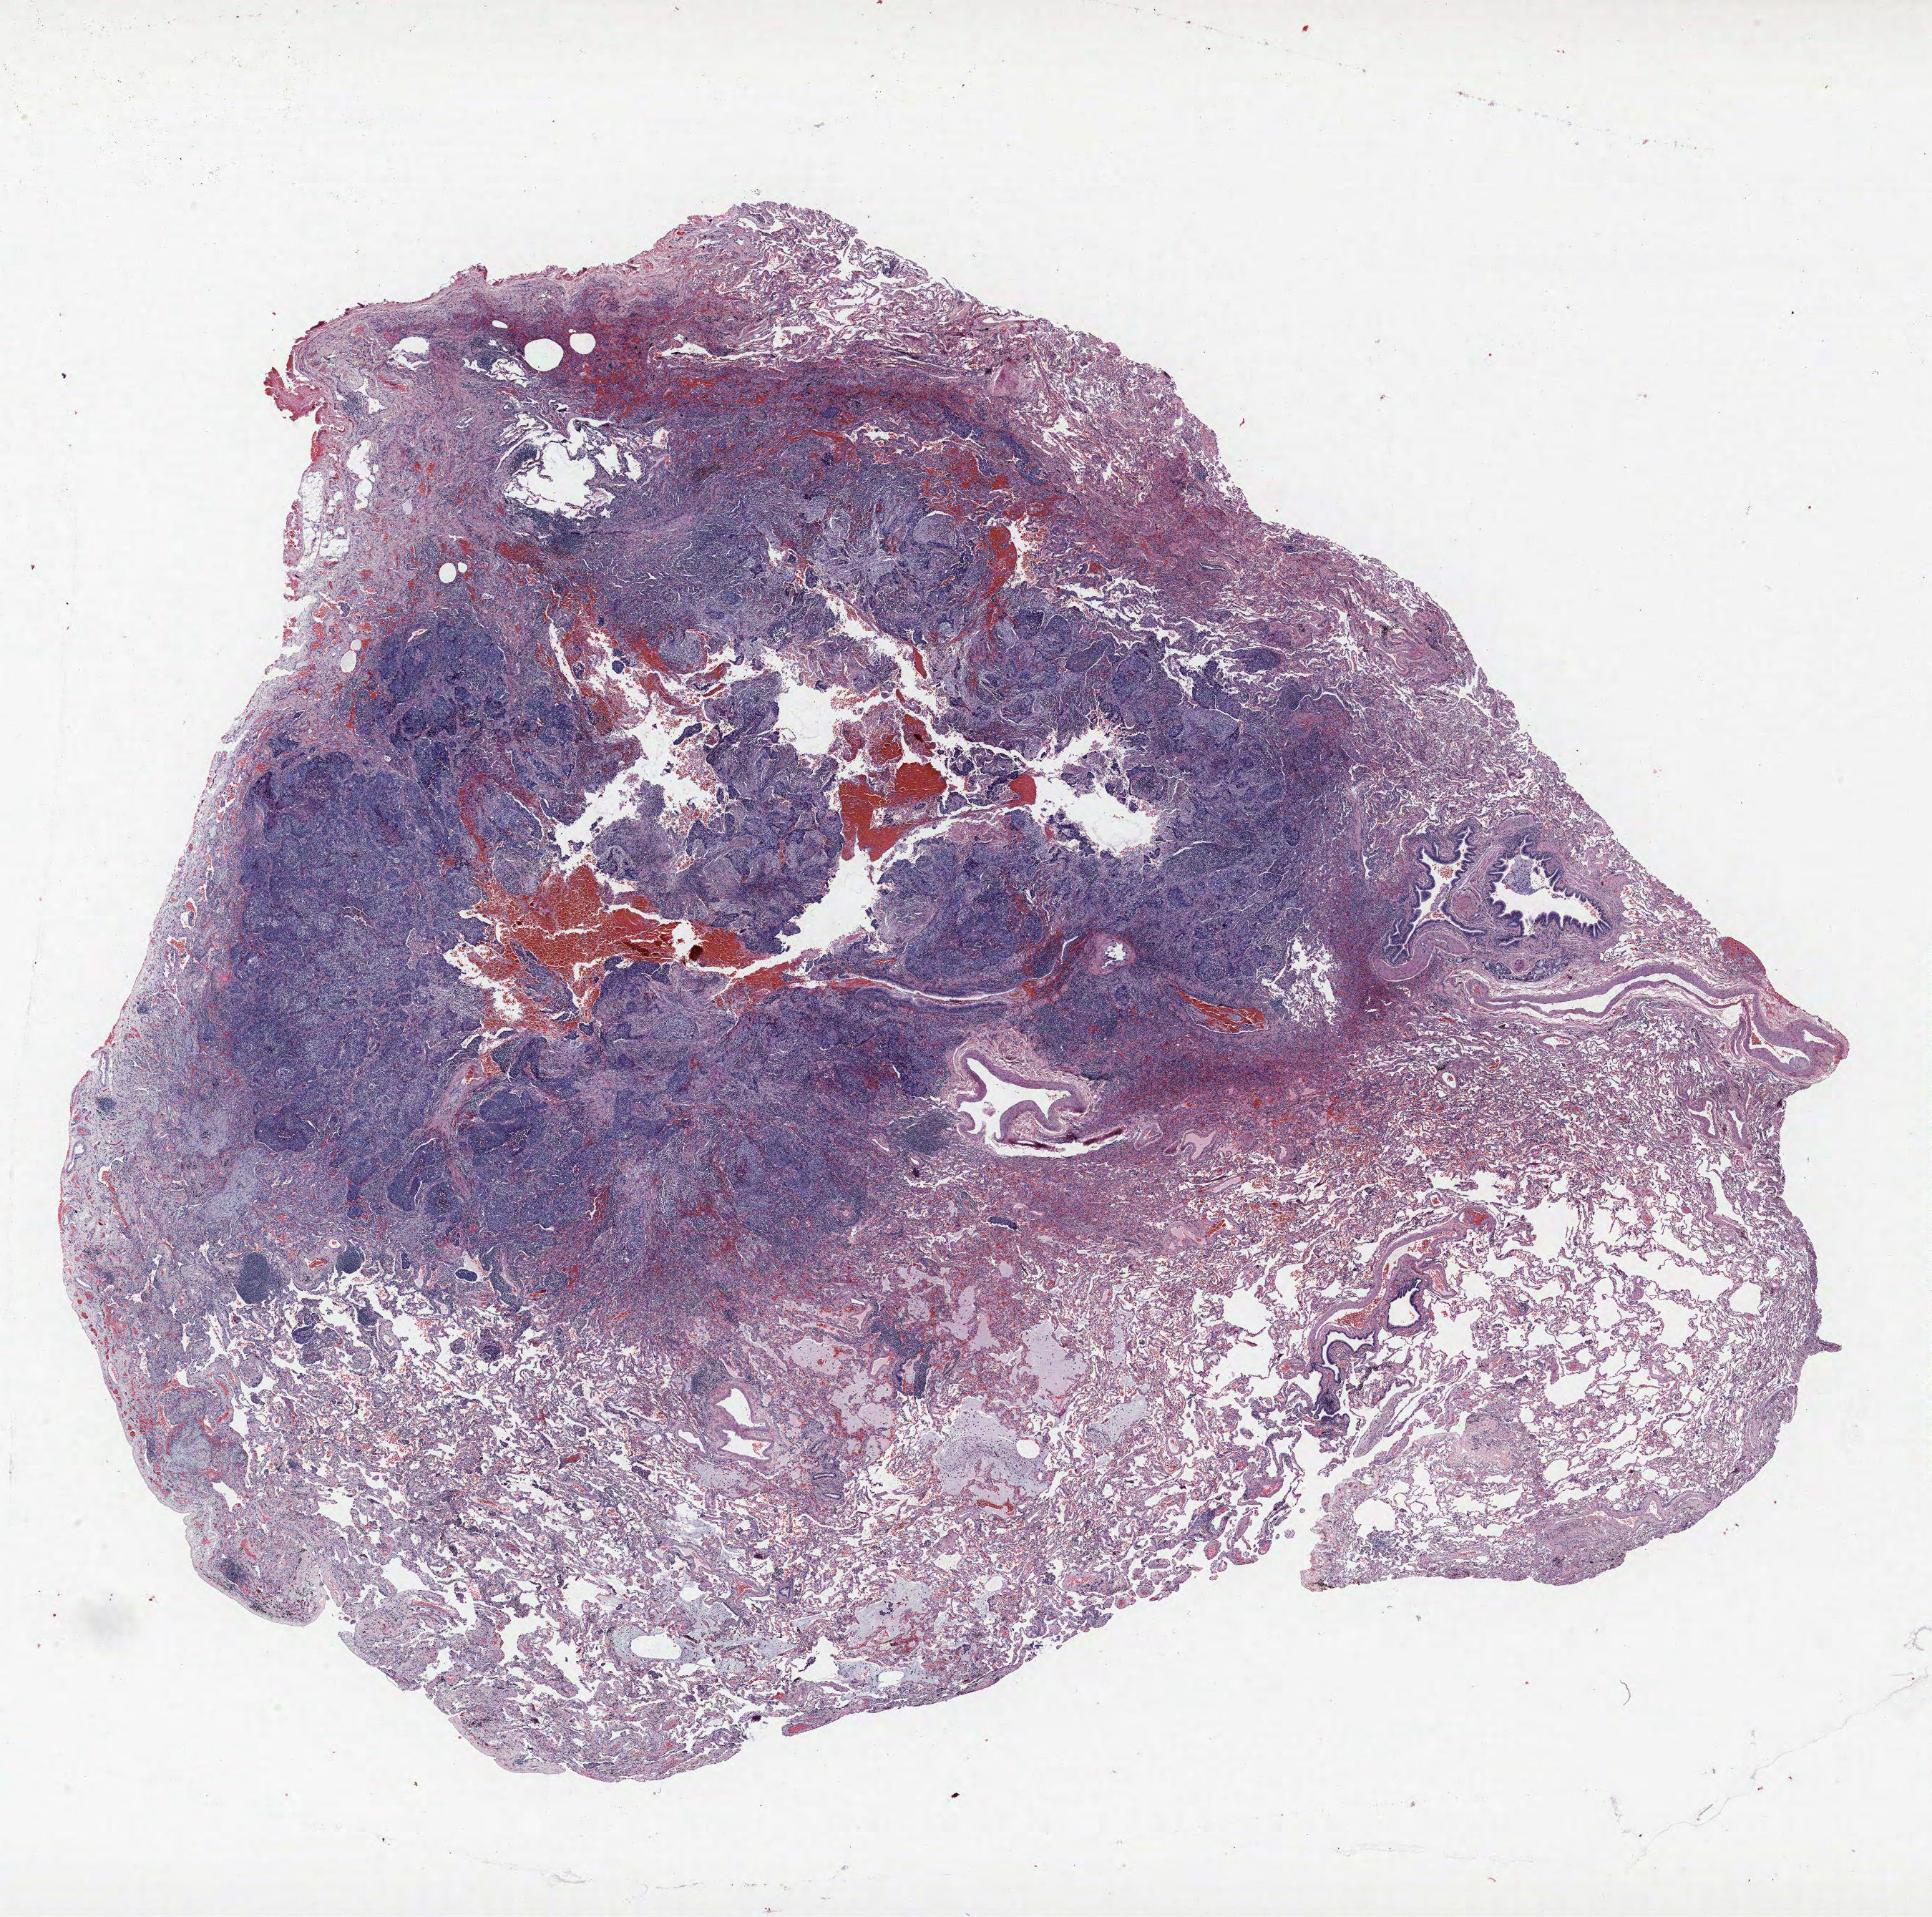
H&E-stained whole-slide image, shown as a low-resolution overview of the whole scanned area (about 21.6 x 21.4 mm). Formalin-fixed paraffin-embedded (FFPE) section. Lung tissue. Male, age 58 at enrolment. Former smoker at enrolment. Grade: moderately differentiated (G2).
* primary tumour location (clinical record): right upper lobe
* stage (AJCC 6th edition): IA
* participant's lung-cancer diagnosis: Squamous cell carcinoma, NOS
* tumour size (pathology): 18 mm